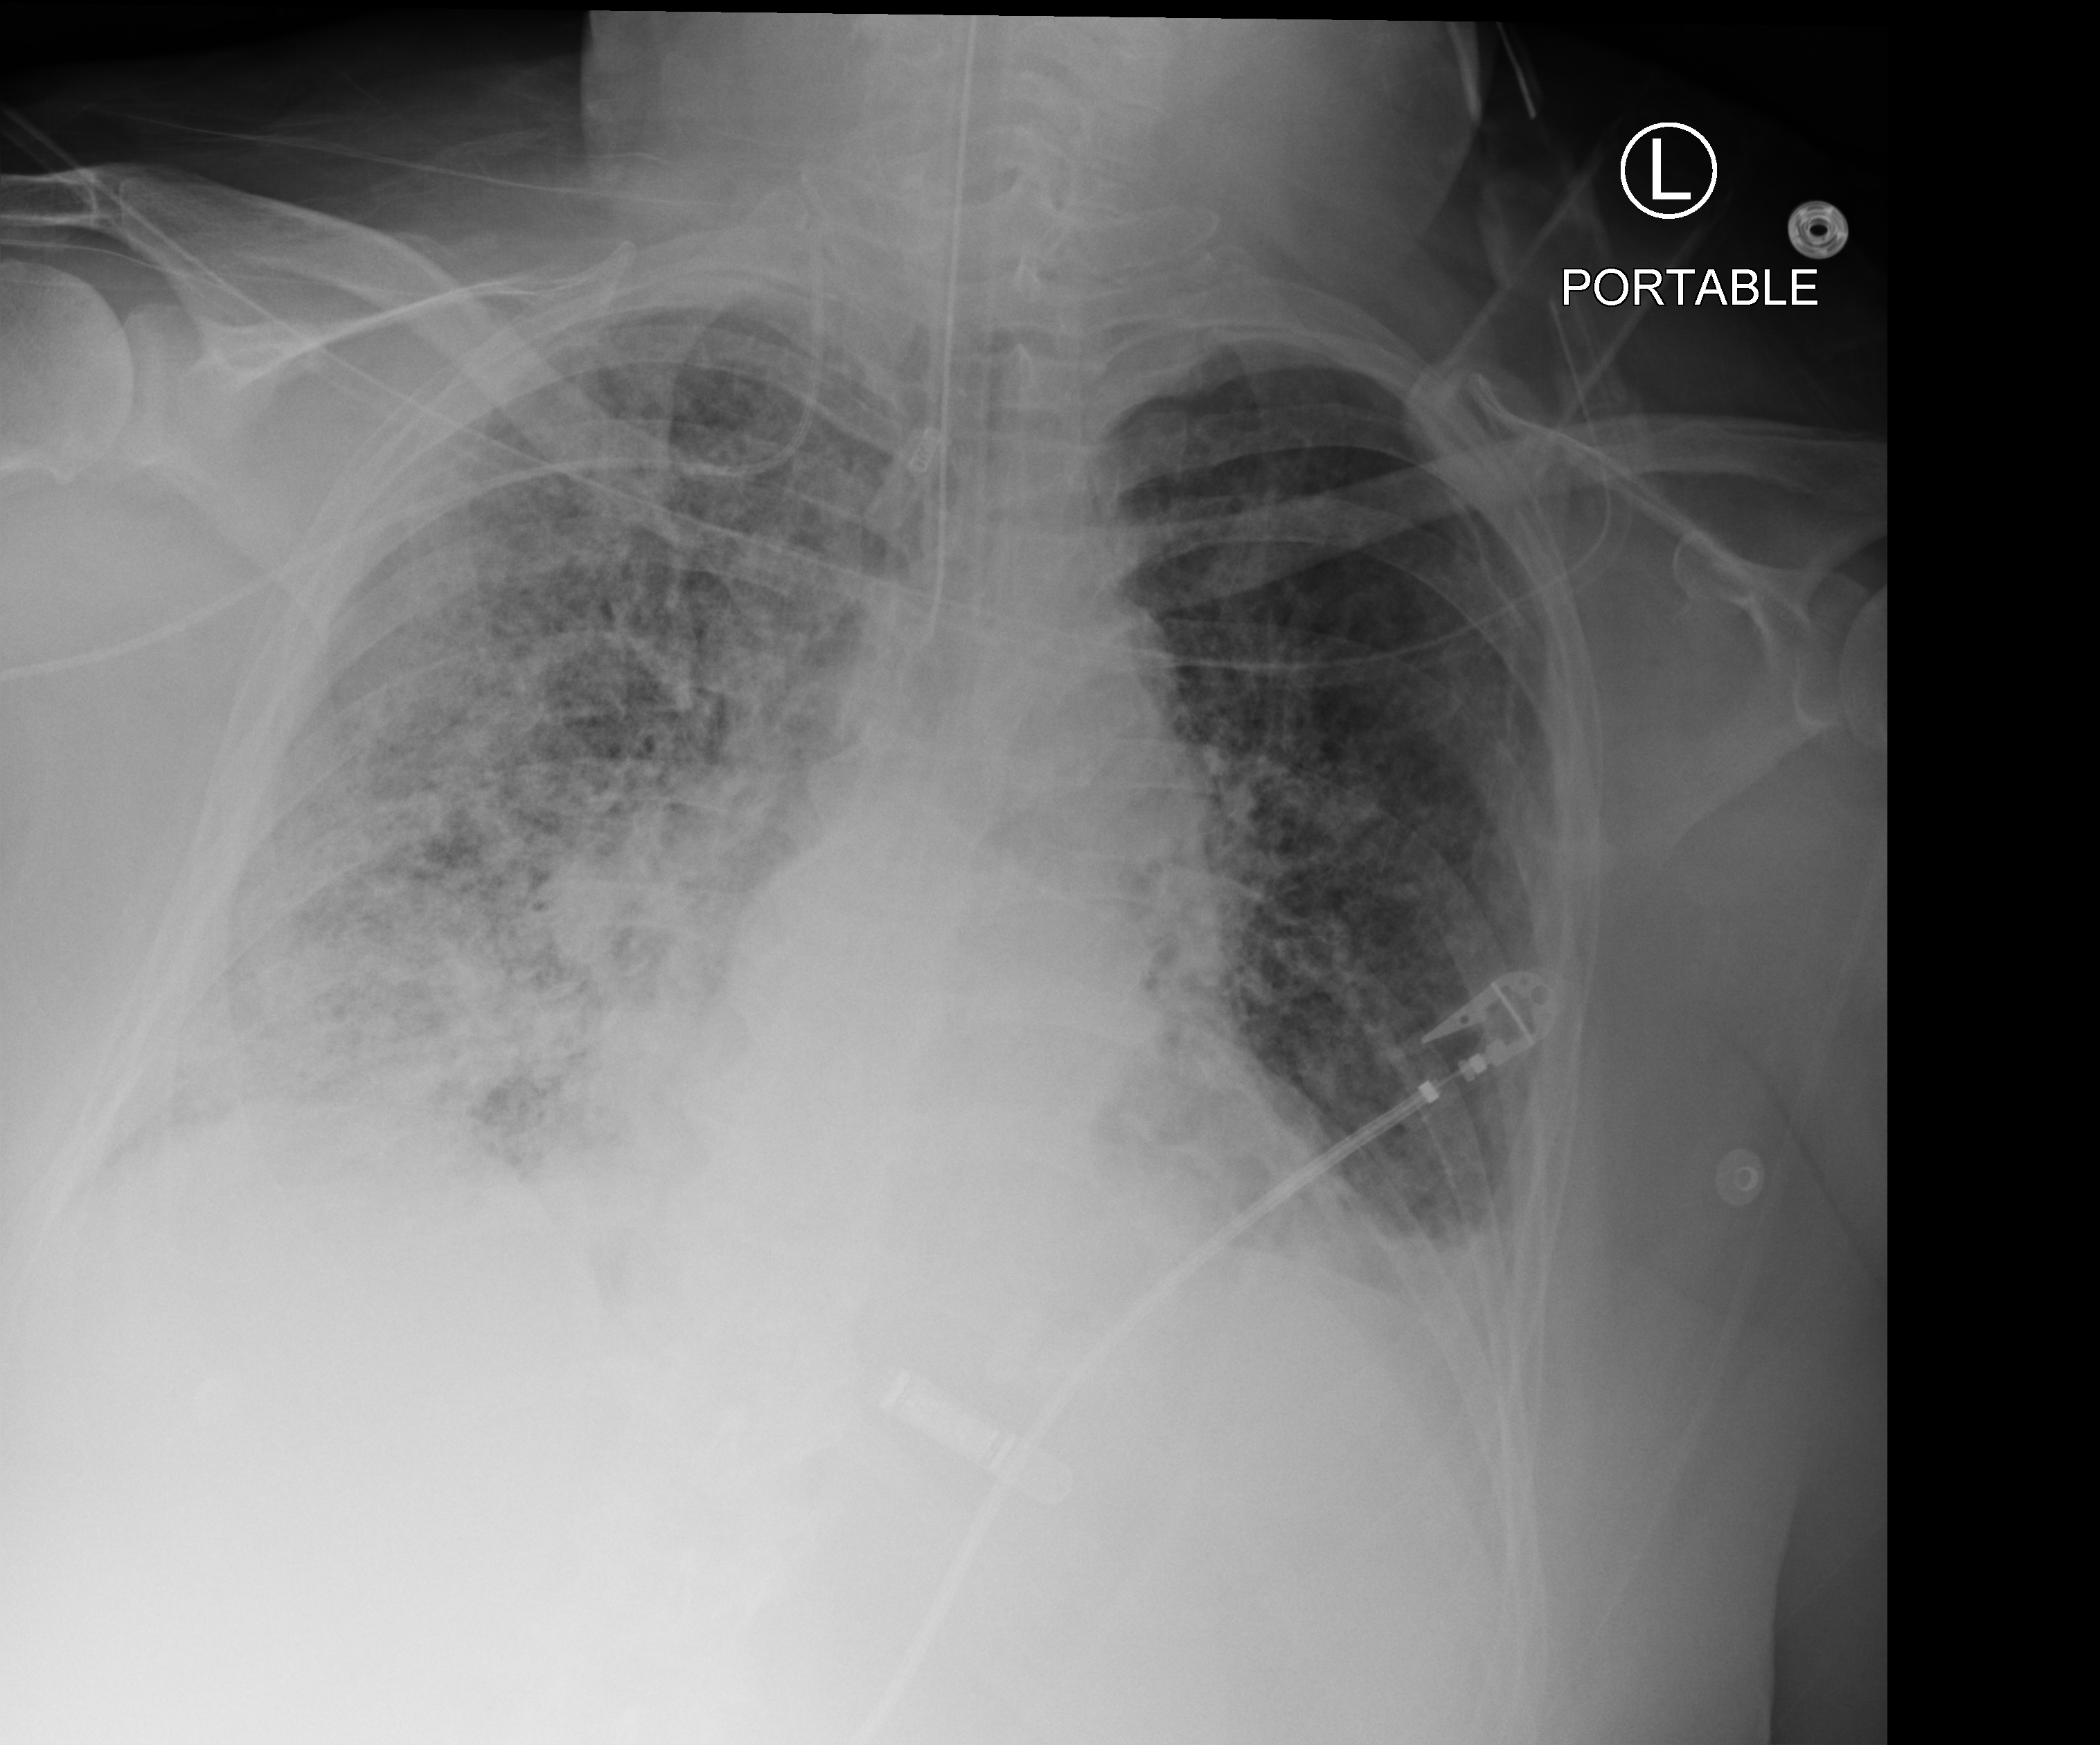
Portable chest radiograph; anteroposterior (AP) projection. Patient hospitalised with COVID-19; female, aged 60–74 years.
Hospital-stay facts (about this admission, not read from this image; timing relative to this image not recorded):
- other chronic lung disease (admission record): yes
- smoking status (admission record): former